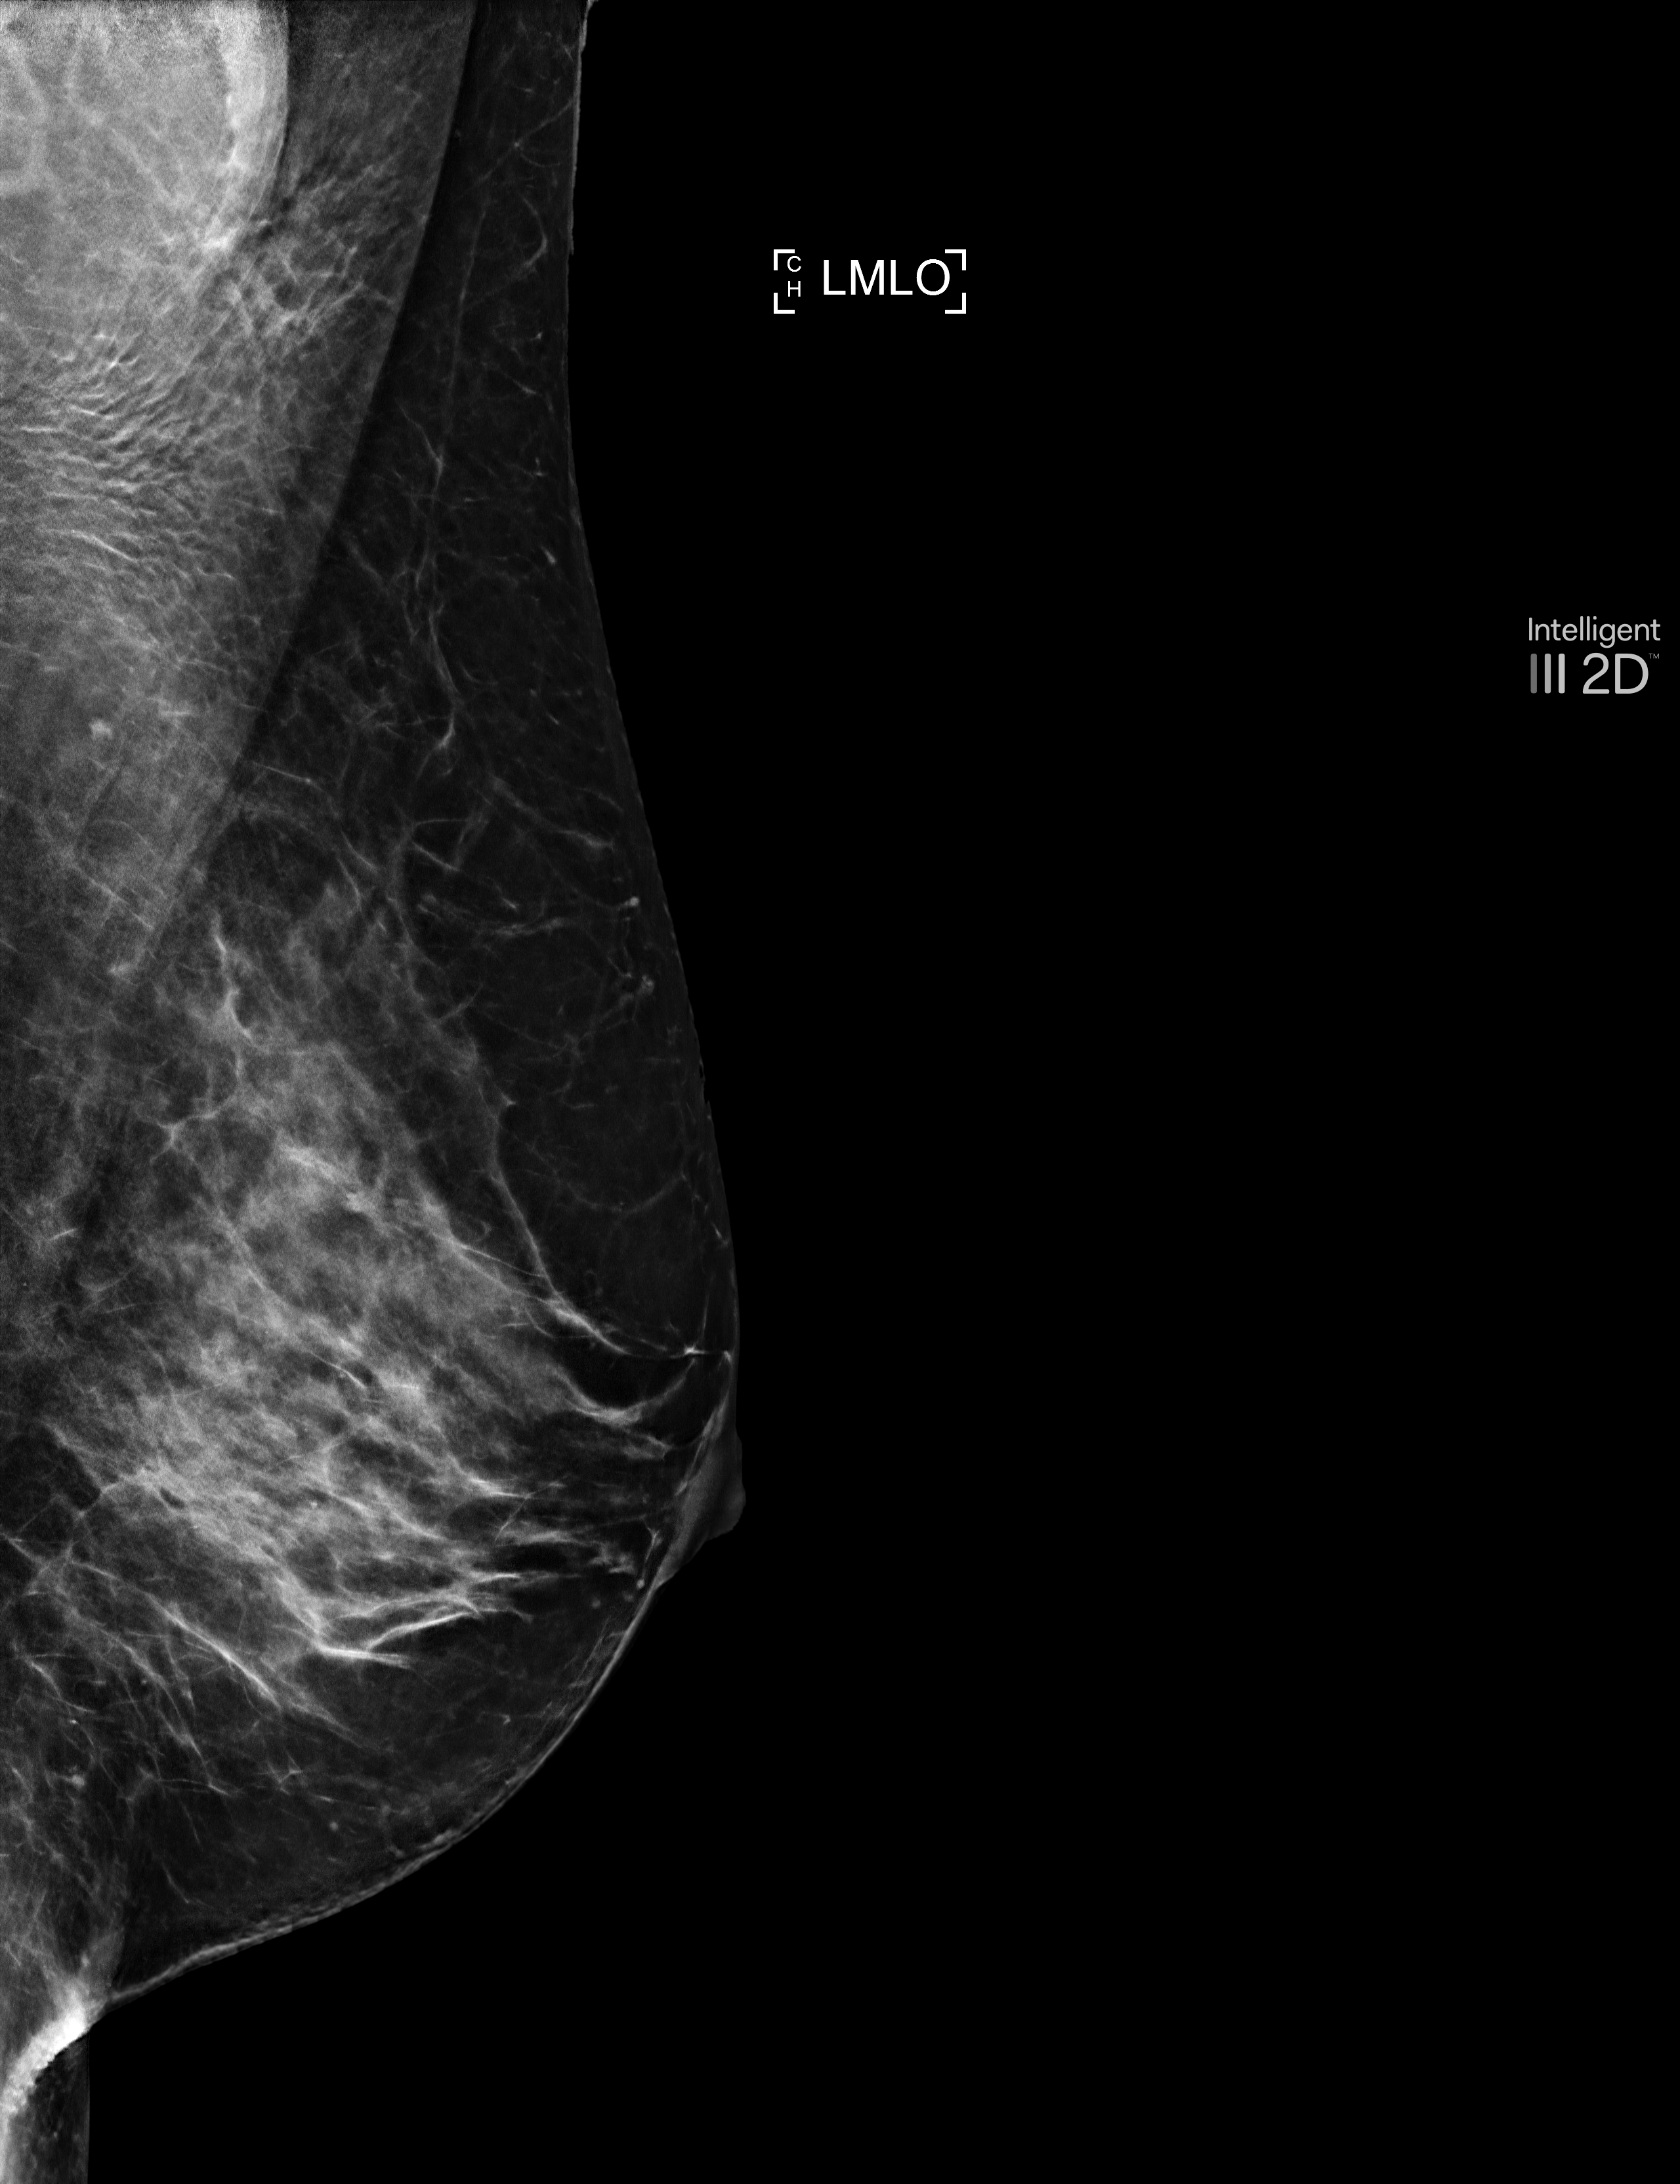
Screening examination, compressed breast thickness 64 mm. Patient: female, 60 years.
Image type: synthesized 2-D view from tomosynthesis. Breast: left. Projection: medio-lateral oblique projection.